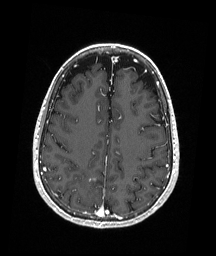
Brain MRI from a brain-tumour surgery series, one axial slice. Position 74 of 192 along the scan axis. T1-weighted post-contrast. 1 mm slice thickness. 216 × 256 image matrix, field of view 211 × 250 mm. From the clinical record (not read from this slice): histopathology: Astrocytoma; WHO grade: 3; IDH mutation: yes.
Structures marked on this image (expert manual segmentation):
- tumour: bounding box [x1, y1, x2, y2] px = [88, 177, 96, 182]